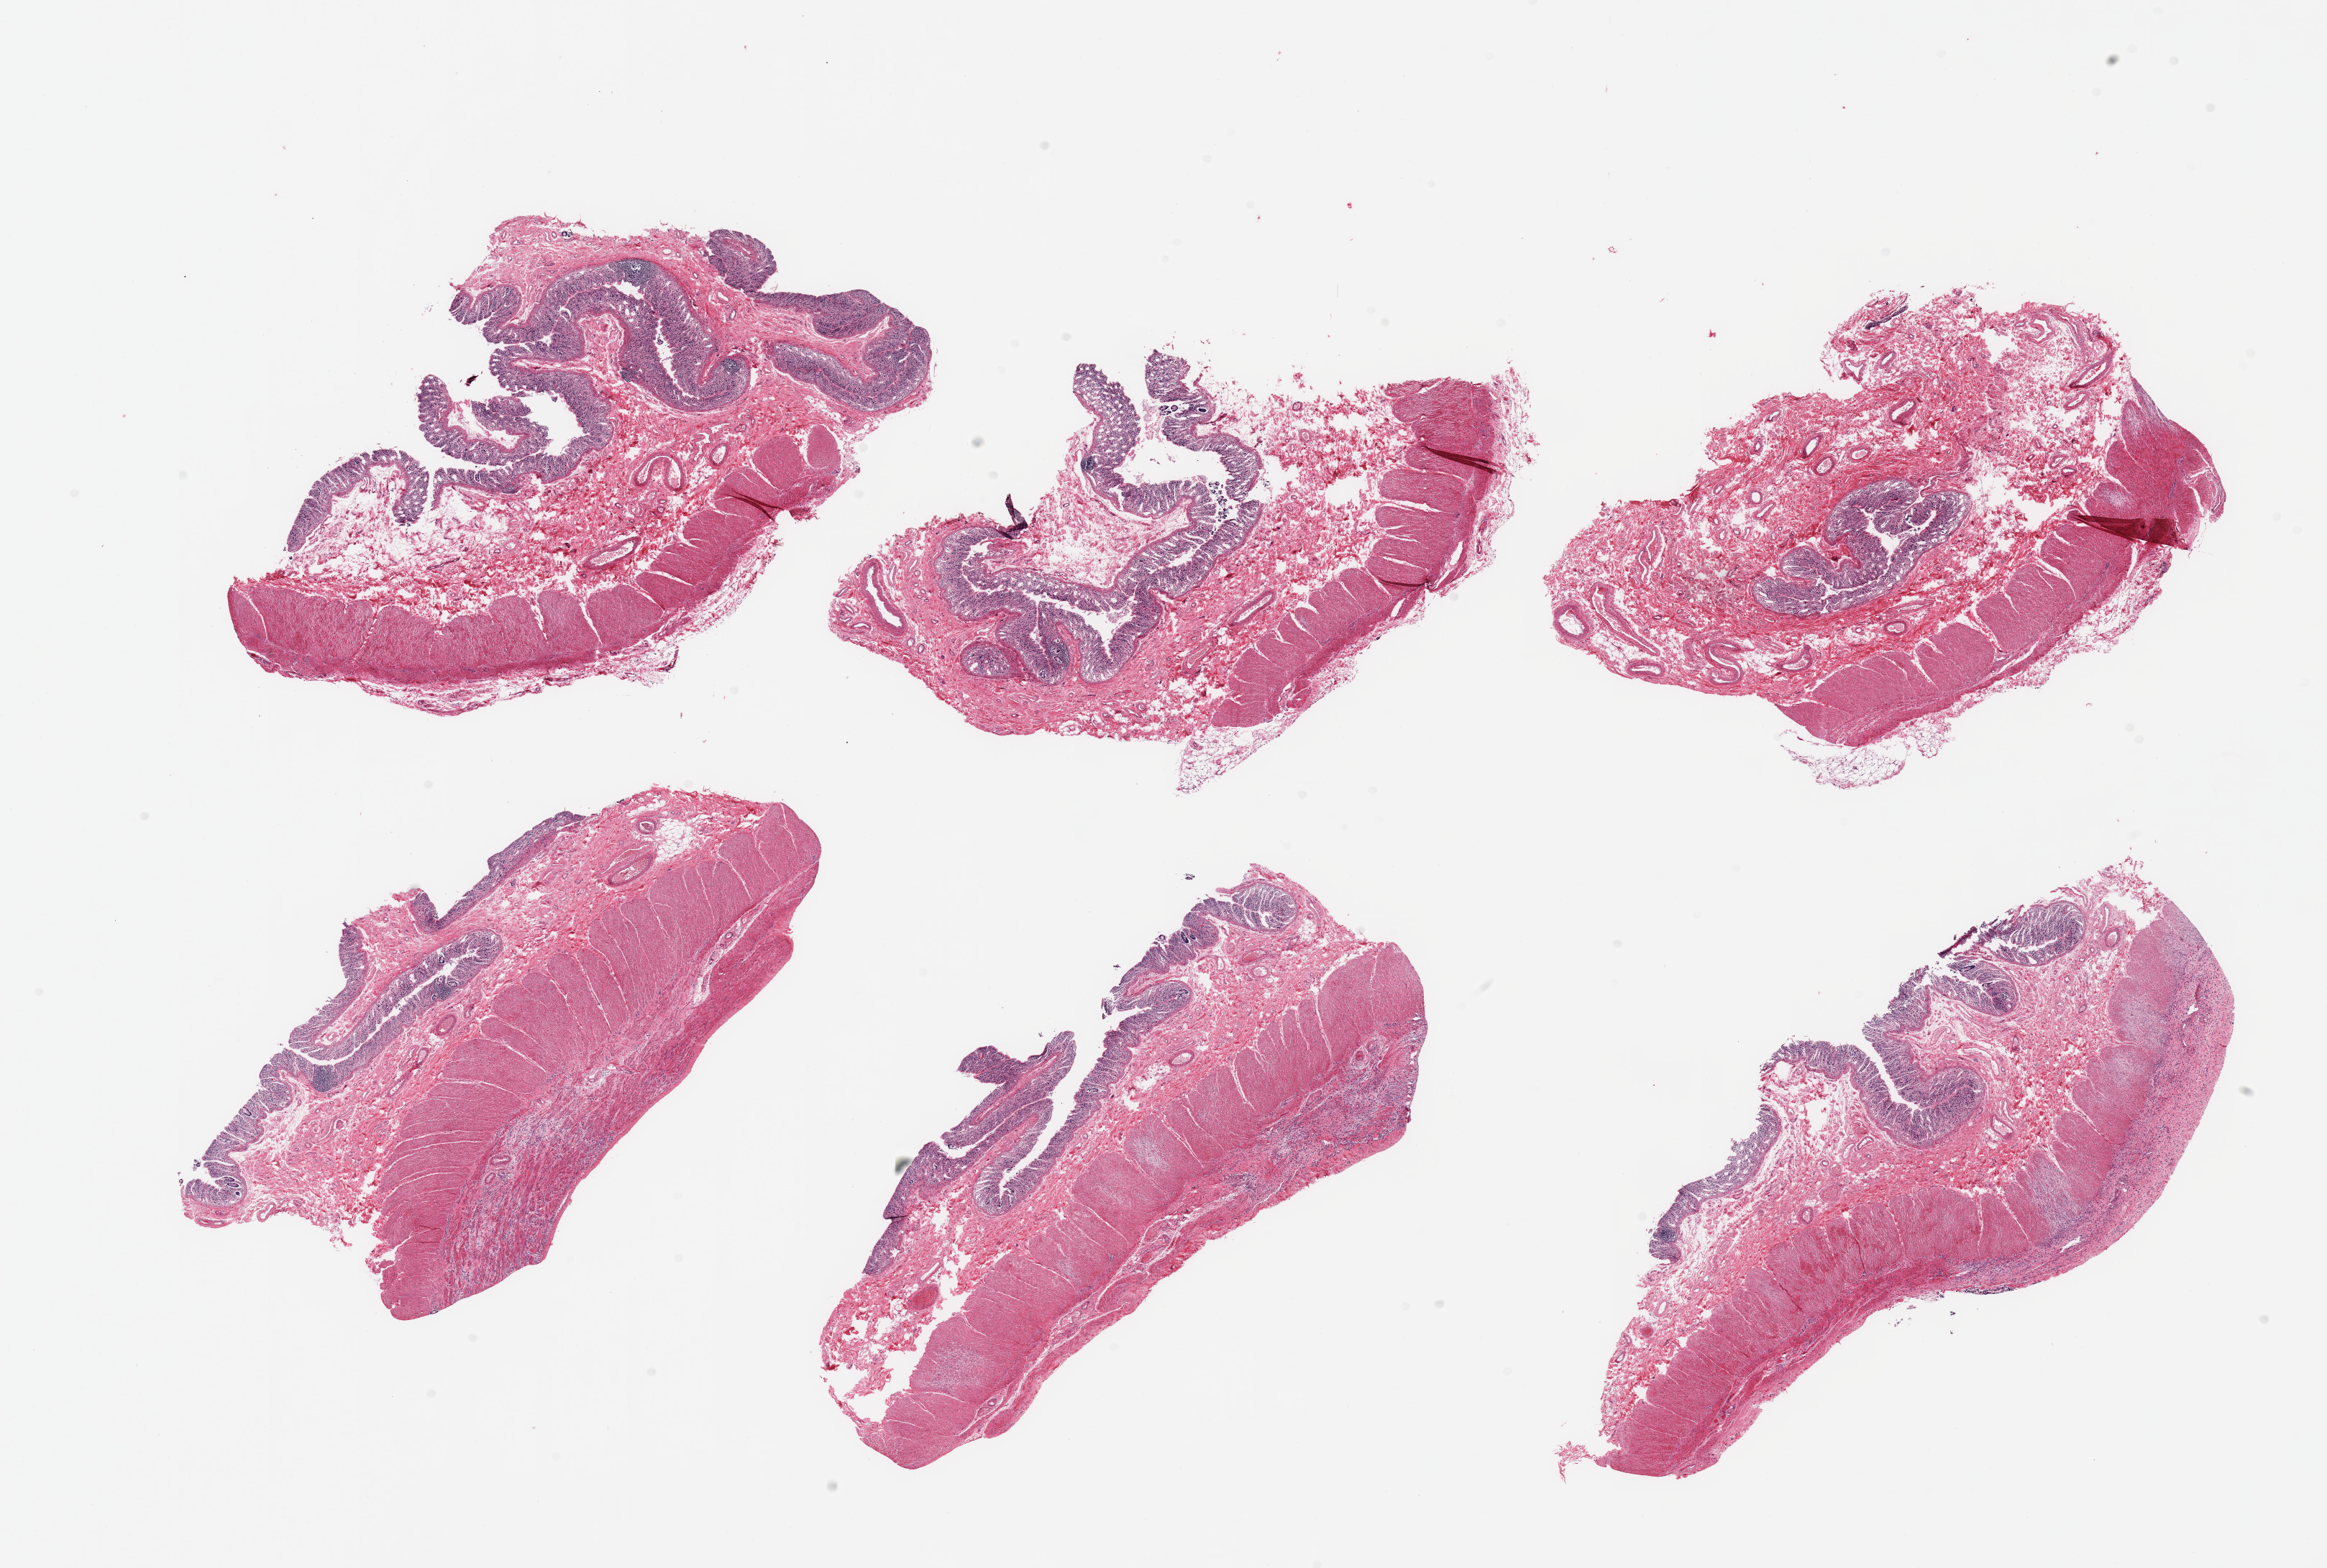
H&E whole-slide image — low-resolution overview of the scanned area, about 25.6 x 17.3 mm. PAXgene-fixed, paraffin-embedded tissue. Sampled site (target tissue): transverse colon. Donor tissue sample. Male donor.
Review note (as recorded): 6 pieces; moderately to severely autolyzed mucosa and well preserved muscularis, serositis.